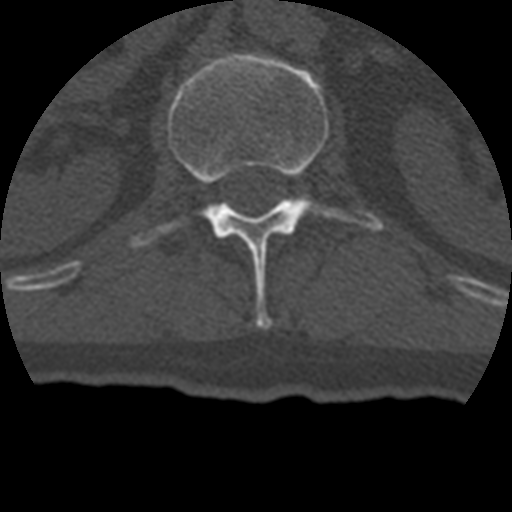
CT including the spine, one axial slice; slice 142 of 399 in the series (ordered by position); bone window (W 1800 / L 400 HU); 1.25 mm slice thickness; 512 × 512 image matrix, field of view 160 × 160 mm. Patient age 69 years. Case-level facts recorded for this patient, not image findings: primary cancer: prostate.
Outlined on this slice (semi-automatic segmentation, software-assisted and operator-edited):
- L1 vertebra: bounding box (x1, y1, x2, y2) in pixels: (131, 53, 383, 329)